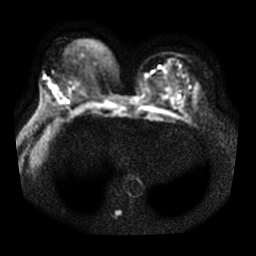
Breast MRI, one axial slice. Diffusion-weighted series; image 2 of 4 stored at this slice position (different b-values; order by instance number). 3 T. 5 mm slice thickness. 256 × 256 image matrix, field of view 340 × 340 mm. Female patient.
Annotated regions visible in this slice (outlined manually by an expert reader):
- tumour on diffusion-weighted imaging: bounding box (x1, y1, x2, y2) in pixels: (50, 84, 53, 88)